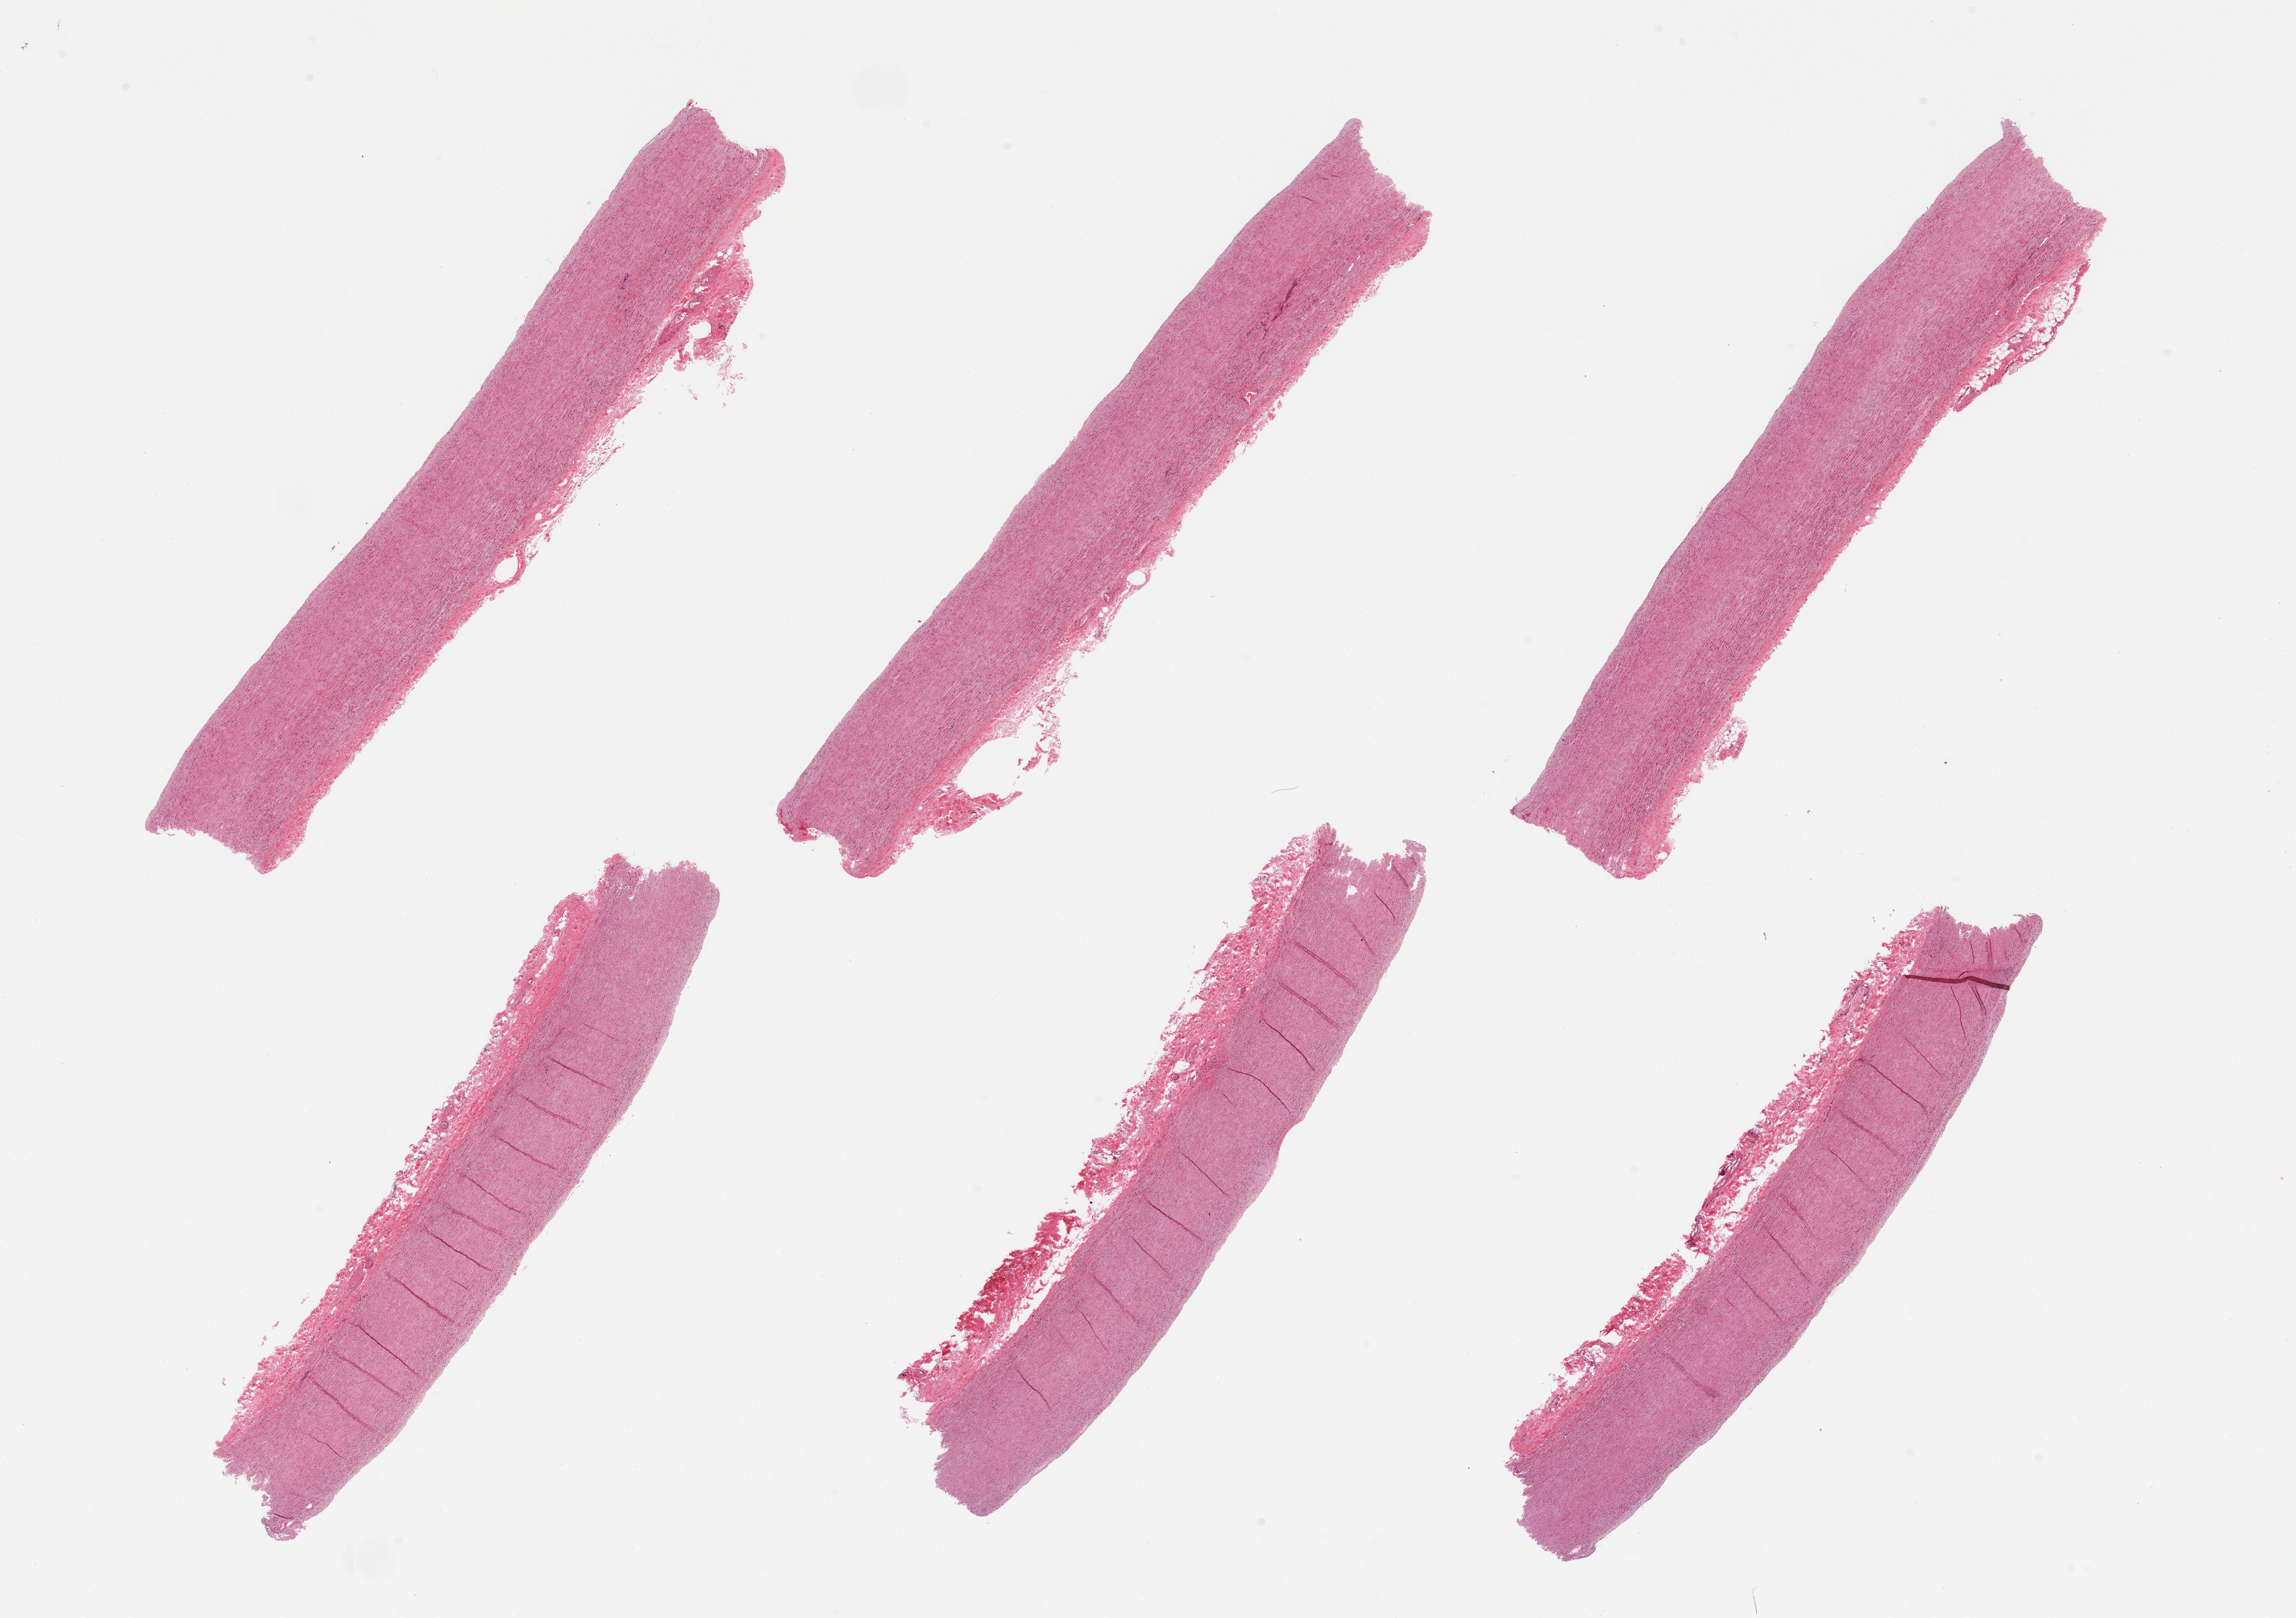
Whole-slide image, haematoxylin and eosin stain — a low-resolution overview of the entire scanned area, about 25.6 x 18.0 mm, PAXgene-fixed paraffin-embedded (PFPE) section, target tissue: aorta, tissue donor sample. Donor sex: male.
Reviewer comment on this tissue sample: 6 pieces; attached adventitia up to 0.6mm.